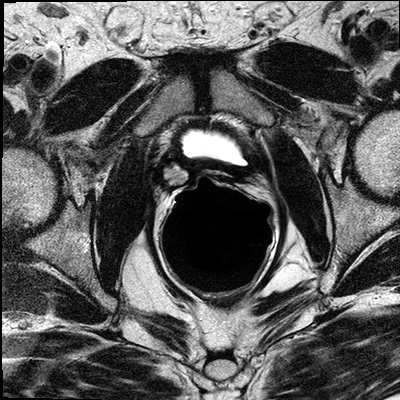
Pelvic MRI after prostatectomy (prostatic bed); 3 images, each a single mid-volume slice chosen by position (not for content).
Image 1: T2-weighted axial slice, slice 19 of 36.
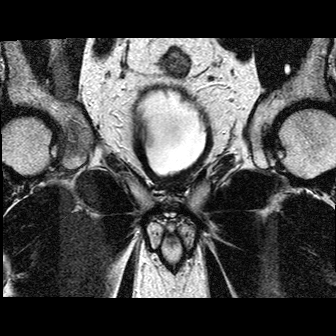
Image 2: T2-weighted coronal slice, series "T2W_TSE_COR", slice 13 of 24.
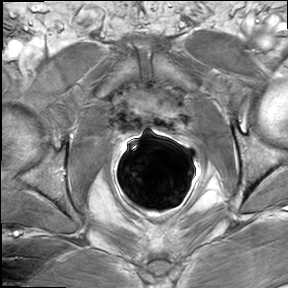
Image 3: axial dynamic contrast-enhanced (DCE) T1-weighted image, series "AX BLISS_GAD", slice 19 of 36, dynamic phase 3 of 5.
Report of this MRI examination:
Regular findings seen within the surgical bed. Multiple surgical clips within the prostatic bed and around the anastomosis. Regular appearance of the anastomosis. No definite masses seen within the prostatic bed. No foci of suspicious enhancement in and around the prostatic bed. Unremarkable urinary bladder and bladder neck. Small seroma posterior lateral to the right bladder neck; just superior to the anastomosis. Remnant left seminal vesicles present Series 601 slice location 69-84. No tumor masses seen within the remnant seminal vesicles or suspicious enhancement, No suspiciously enlarged obturator and iliac lymph nodes. Several small lymph nodes seen along the iliac vessel, the largest located just below the bifurcation median presacral measuring 8 x 6 mm without MRI visible fatty hilum ( series 701 slice location 126) The largest obturator nodes measures 3-4 mm. The visualized osseous structures without evidence of involvement. IMPRESSION: 1) remnant left seminal vesicles, without evidence of malignancy. 2) No suspicious masses. 3) No enlarged obturator or iliac lymph nodes, with one presacral (median line) lymph node just below the bifurcation measuring 8 x 6 mm, without distinct fatty hilum. This is of uncertain significance. 4) Normal appearance of the prostatic bed and anastomosis, with expected post surgical changes (including a small seroma).

Prostatectomy specimen pathology (as recorded; the prostatectomy preceded this MRI, which images the post-surgical bed):
PROSTATE Gross Description The specimen is received in a single container labeled with the patient's name, hospital number and "Prostate". The specimen consists of a prostatectomy specimen weighing 35.8 grams and measuring 4.5 cm right to left, 3.2 cm anterior to posterior, and 3.5 cm superior to inferior. A stump of left seminal vesicle is present measuring 1.5 x 1 x 0.5 cm. The left vas deferens is also present measuring 2.5 cm in length and 0.3 cm in diameter. The right seminal vesicle measures 3.5 x 1 x 0.5 cm and appears complete. The right vas deferens measures 3 cm in length and 0.3 cm in diameter. External surface is smooth. The right side is inked black and the left side is inked blue. Representative sections are submitted in cassettes as follows: 1 basal margin entirely submitted in sagittal sections, 2 and 3 apical margin entirely submitted in sagittal sections, 4 left seminal vesicle, basal margin and left vas deferens margin, 5 right seminal vesicle, basal margin and right vas deferens margin, 6 thru 12 left anterior lobe entirely submitted, 13 thru 18 left posterior lobe entirely submitted, 19 thru 22 right anterior lobe entirely submitted, and 23 thru 27 right posterior lobe entirely submitted.
Final Diagnosis
PROSTATE (35.8 Grams) : PROSTATIC ADENOCARCINOMA CONVENTIONAL TYPE. GLEASON GRADE 3+3 SCORE = 6/10. THE TUMOR IS CONFINED TO THE PROSTATE GLAND AND IS BILATERAL WITH PRIMARY INVOLVEMENT OF THE LEFT LOBE. THE TUMOR OCCUPIES 20% OF THE TOTAL GLAND.
EXTRAPROSTATIC EXTENSION IS NOT NOTED. INVASION OF SEMINAL VESICLES IS NOT IDENTIFIED.
PERINEURAL INVASION IS PRESENT. LYMPHOVASCULAR SPACE INVASION IS ABSENT. THE SURGICAL MARGINS ARE NEGATIVE. LYMPH NODE SAMPLING: NO LYMPH NODES PRESENT. TREATMENT EFFECT ON CARCINOMA: NOT APPLICABLE. ADDITIONAL PATHOLOGIC FINDINGS: HIGH GRADE PROSTATIC INTRAEPITHELIAL NEOPLASIA, CHRONIC INFLAMMATION AND NECROTIZING GRANULOMAS (Slides 9 and 14). SEE NOTE. AJCC PATHOLOGIC STAGING: (pT2c, pNx, pMx).
Clinical diagnosis and History: PSA 12.7 ng/ml